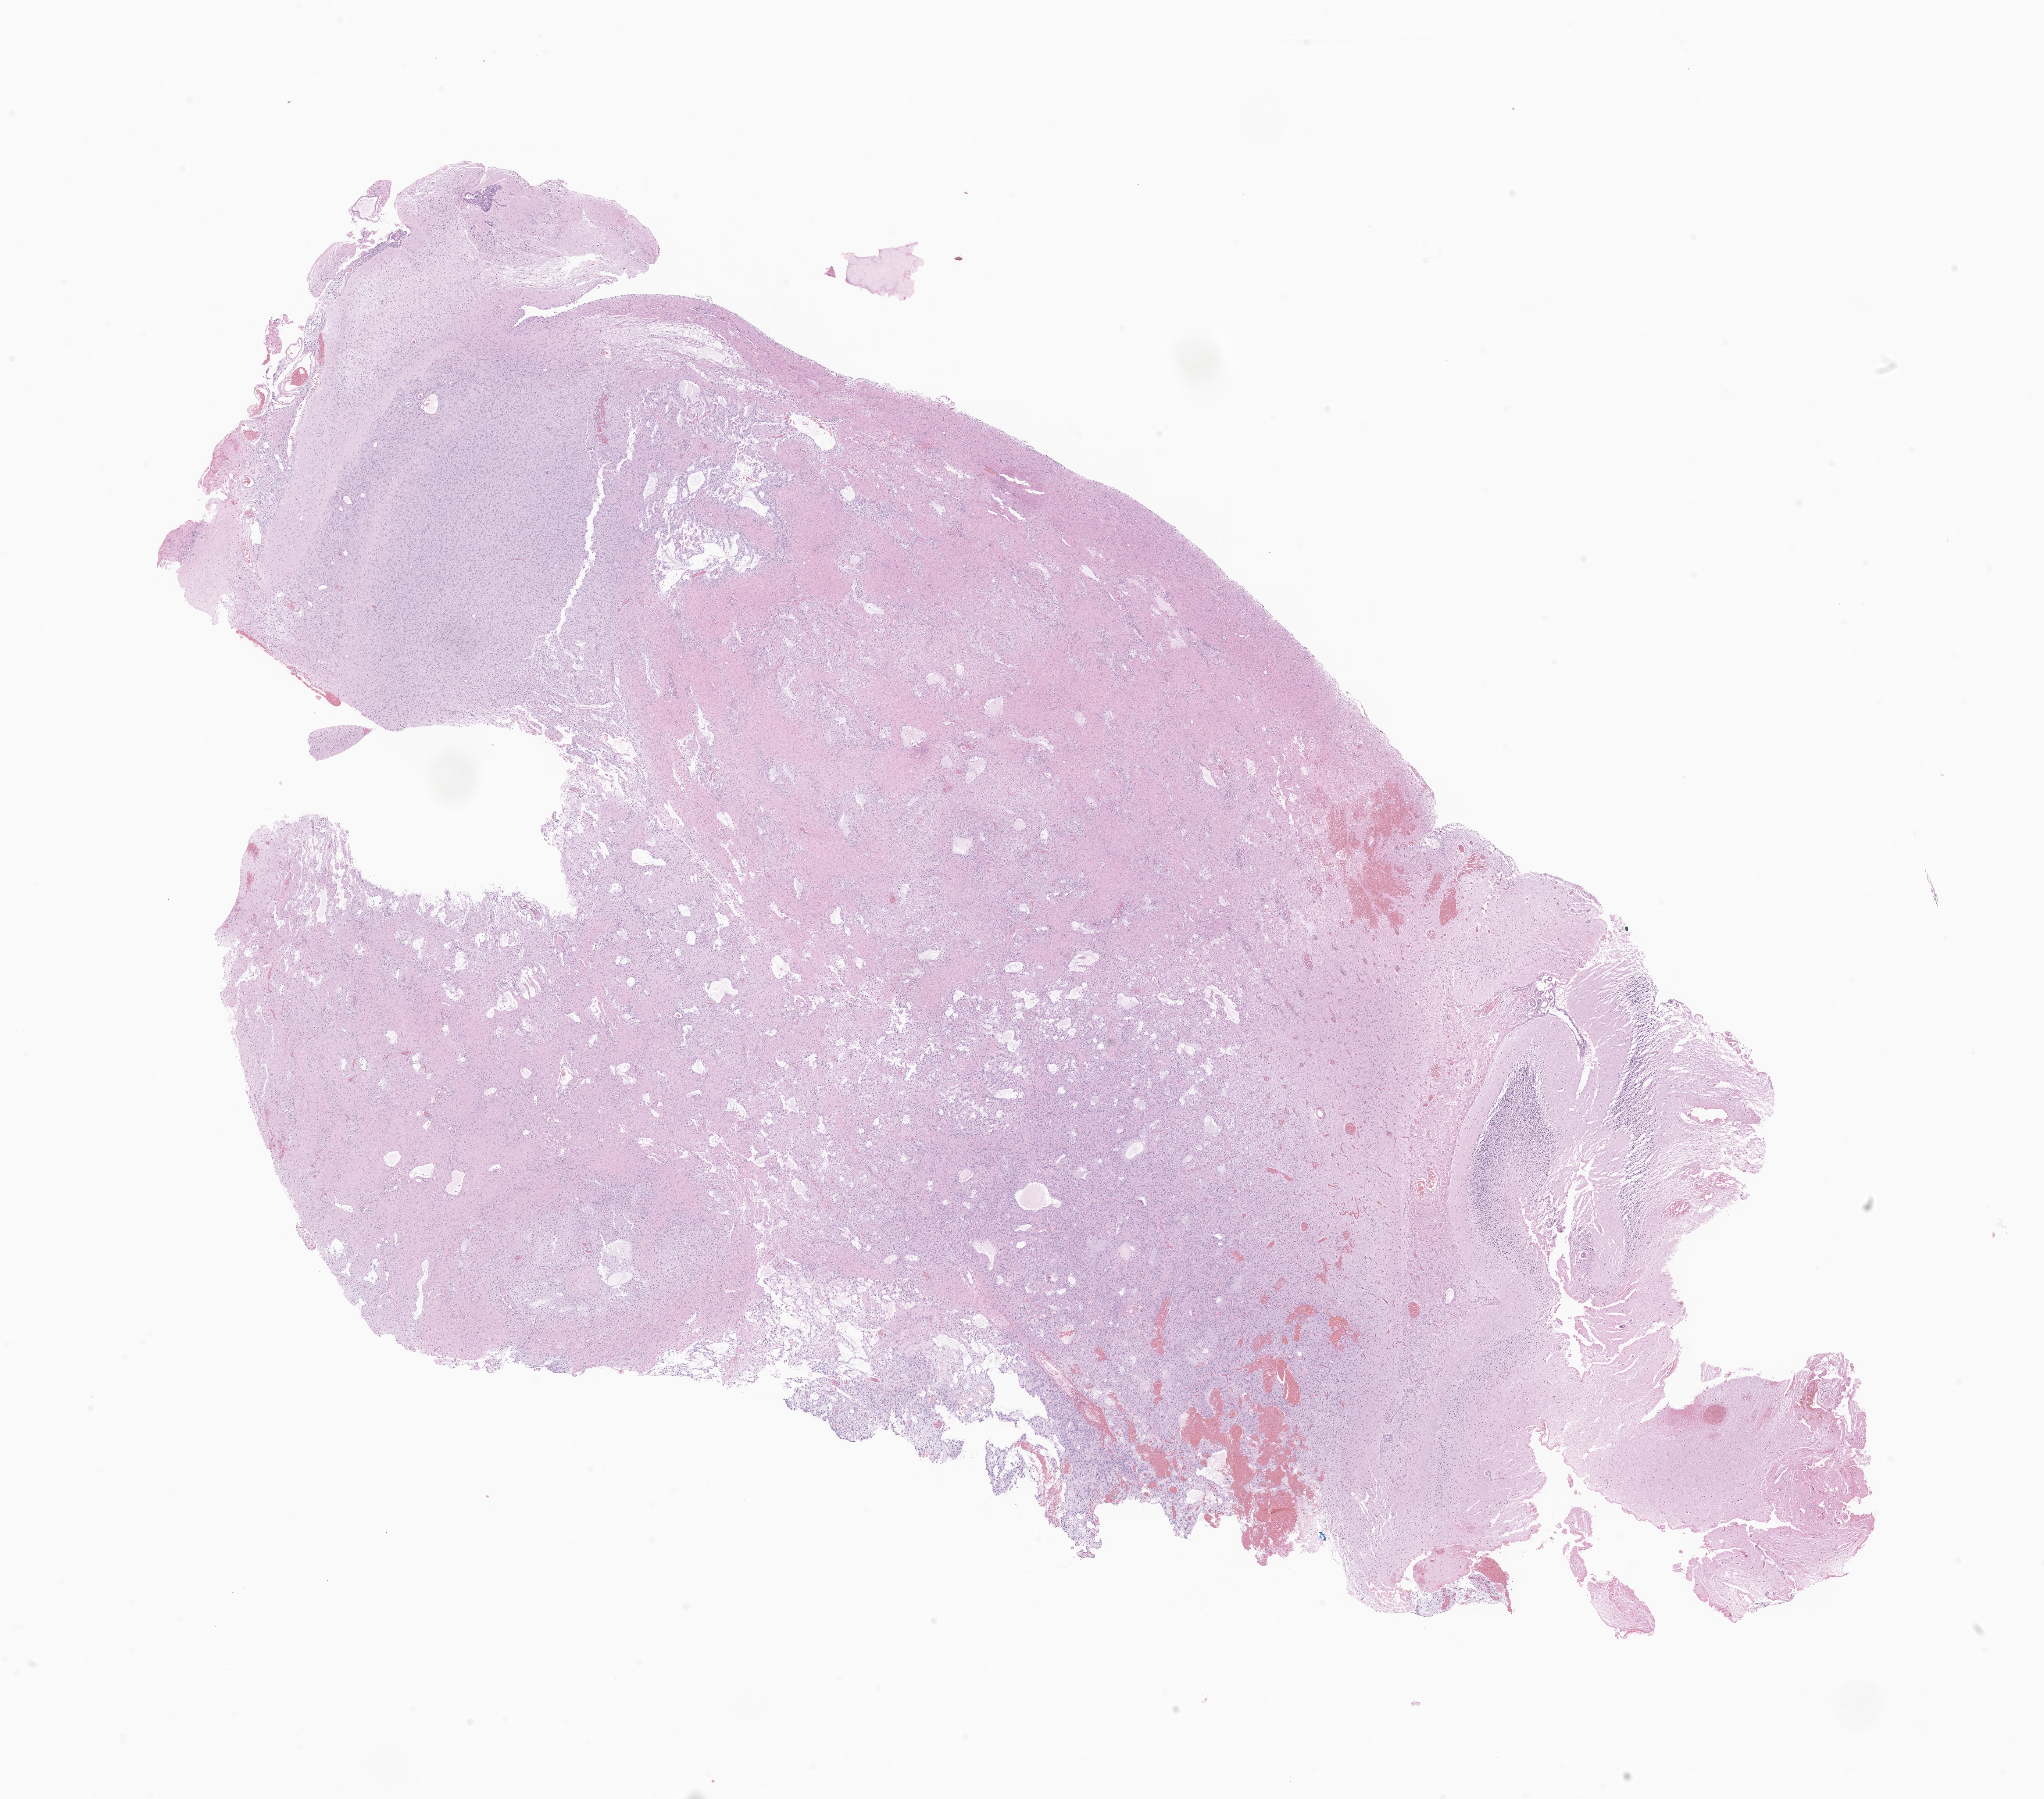
Haematoxylin and eosin whole-slide image of tumor tissue from the brain, whole scanned area (about 23.4 x 20.6 mm) shown as a low-resolution overview. Formalin-fixed paraffin-embedded section. Patient: female, age 128 months.
Diagnosis (ICD-O-3 morphology term): Neoplasm, uncertain whether benign or malignant.